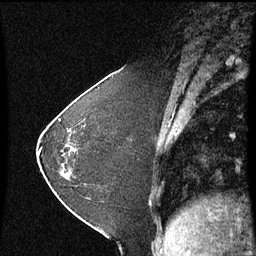
Breast MRI (dynamic contrast-enhanced), one sagittal slice. Slice 23 of 60 in the series (ordered by position). Dynamic contrast-enhanced series, image 2 of 3 at this slice position (ordered by acquisition). 1.5 T. TE 4.2 ms, TR 8.9 ms. 2 mm slice thickness. 256 × 256 image matrix. Female patient, age 37 years. From the clinical record (not read from this slice): setting: breast cancer imaged before/during neoadjuvant chemotherapy; receptor status: HR-positive, HER2-negative.
Outlined on this slice (semi-automatically segmented with operator editing):
- analysis volume of interest (the breast-tissue region the enhancement analysis was run in; not a lesion): bounding box <60,102,122,181> (left, top, right, bottom; pixels)
- tumour enhancement mask (voxels above the 70 % enhancement threshold inside the analysis volume of interest): <60,120,71,133>